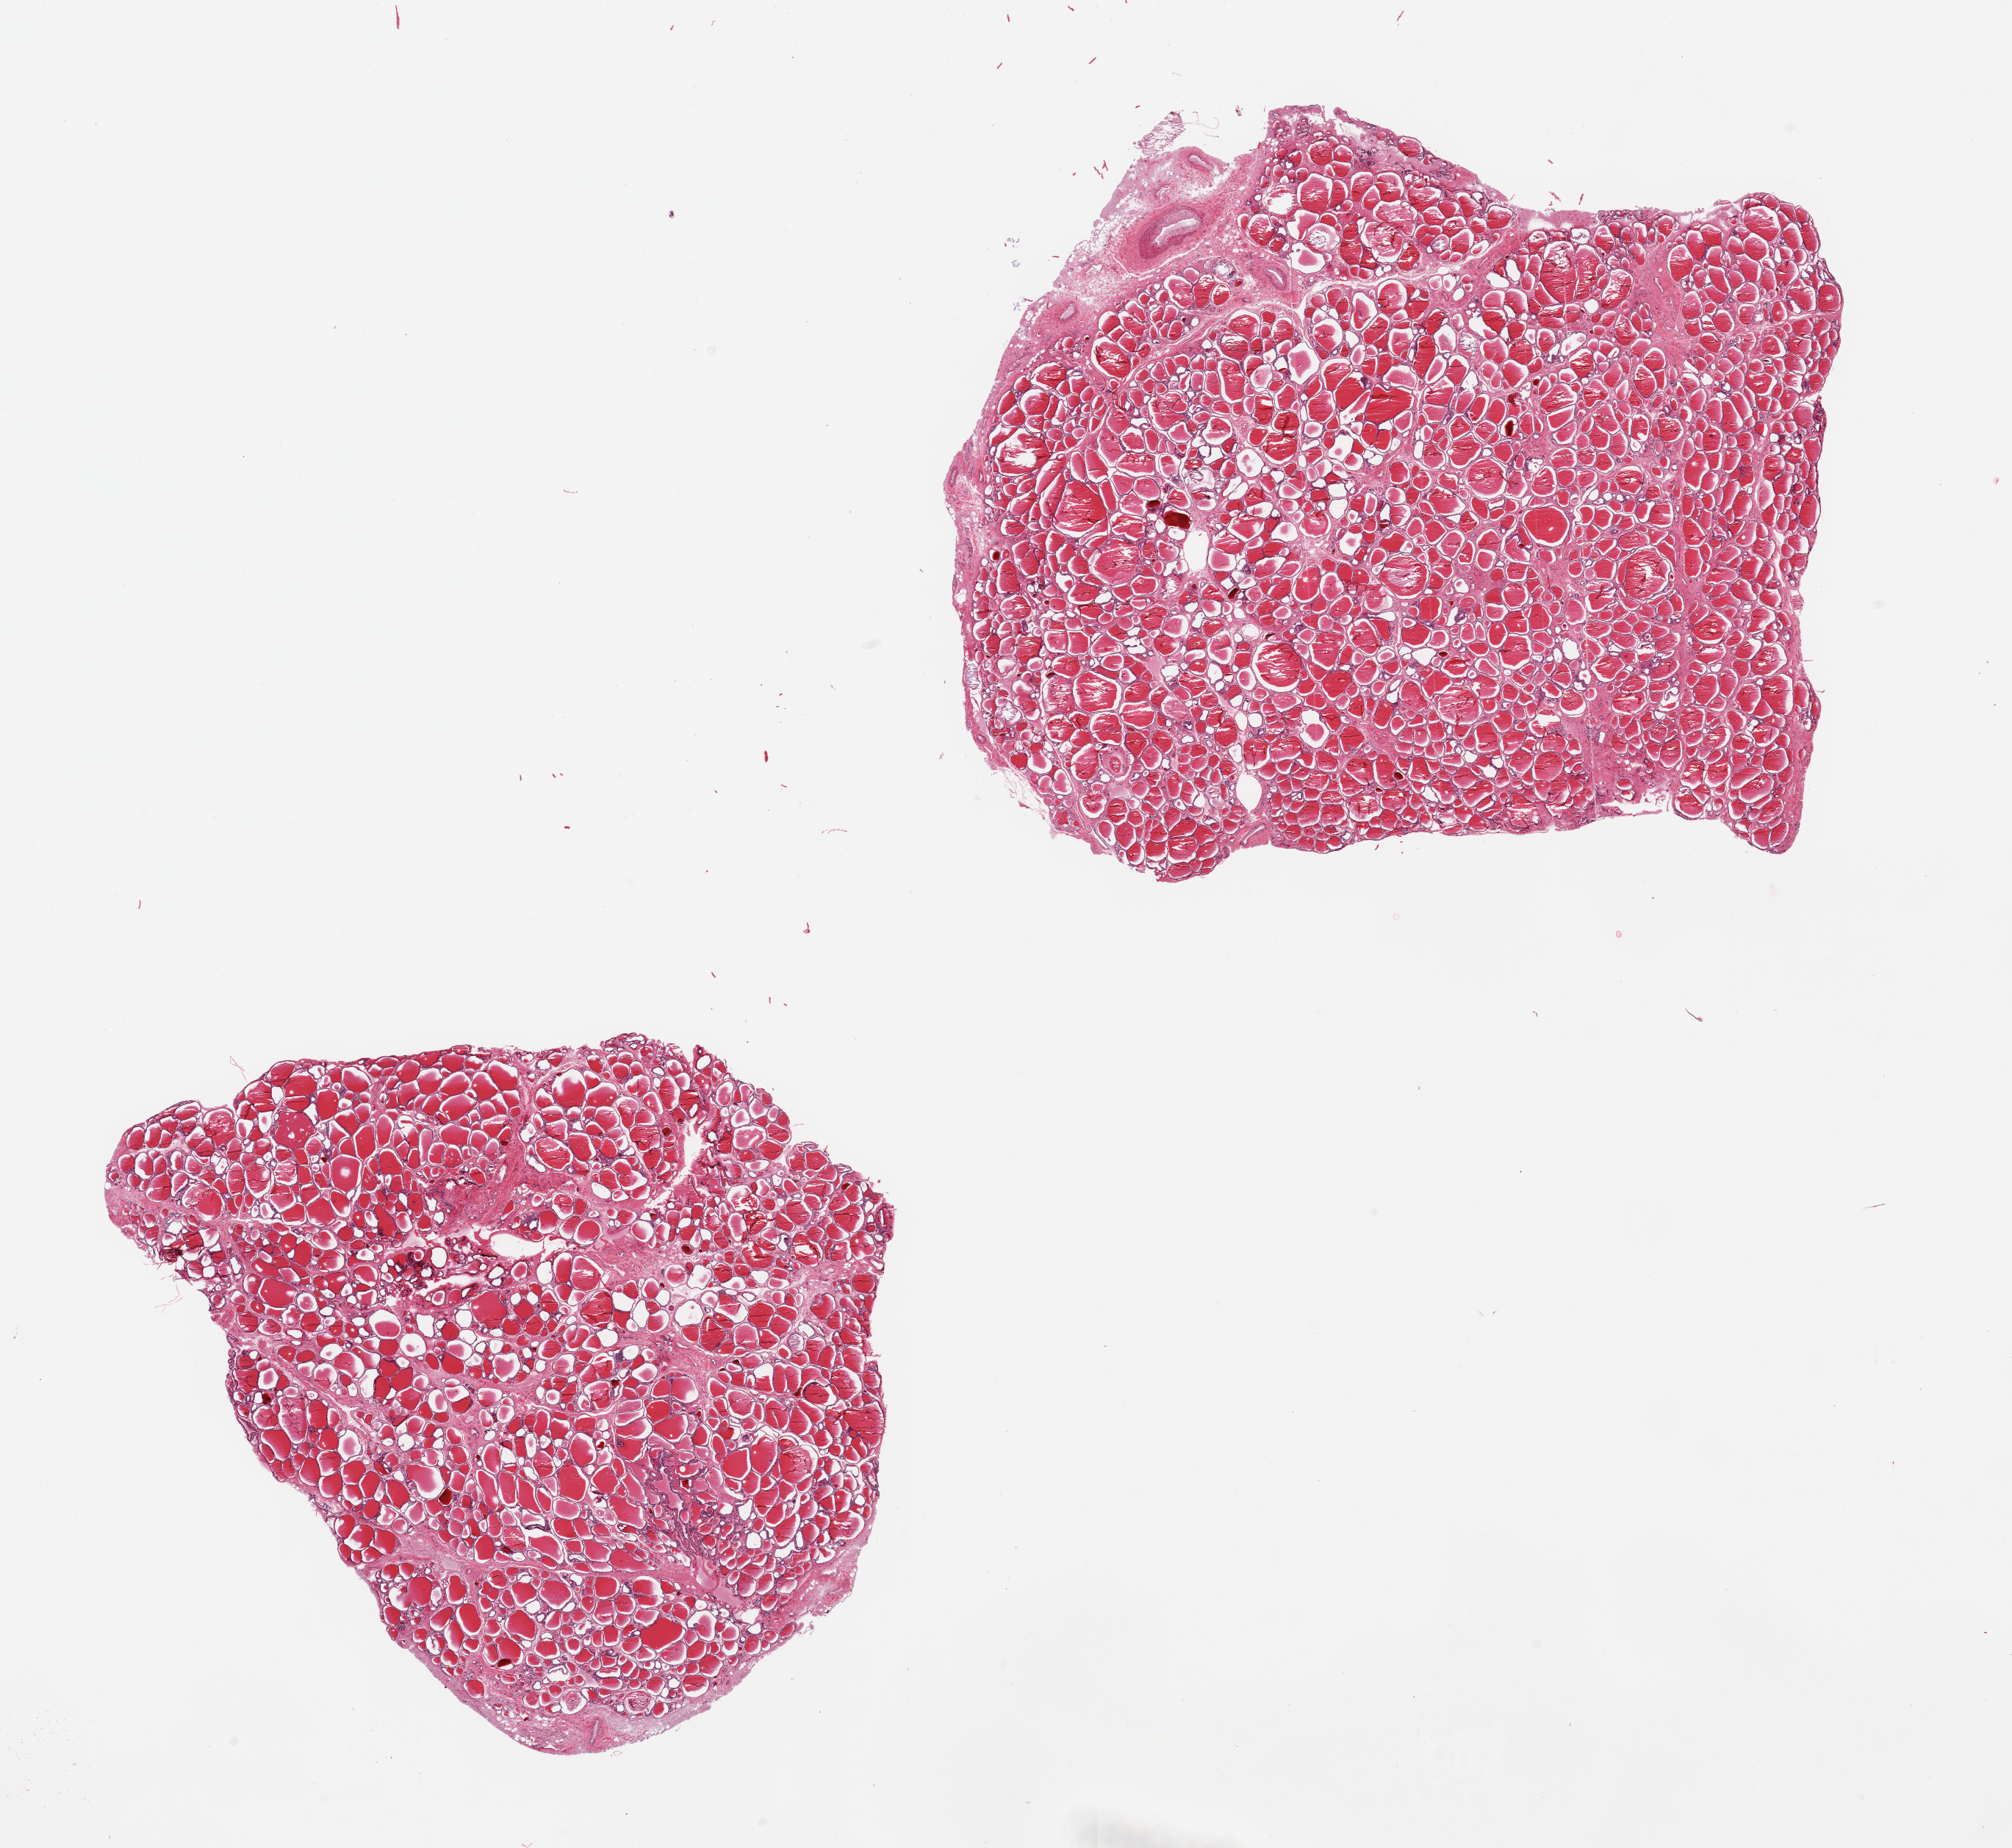
Hematoxylin and eosin (H&E) whole-slide image, brightfield, a low-resolution overview of the entire scanned area, about 21.7 x 19.9 mm; PAXgene-fixed paraffin-embedded (PFPE) section; sampled site (target tissue): thyroid; tissue donor sample. Female donor.
• pathologist's review note for this sample: 2 pieces